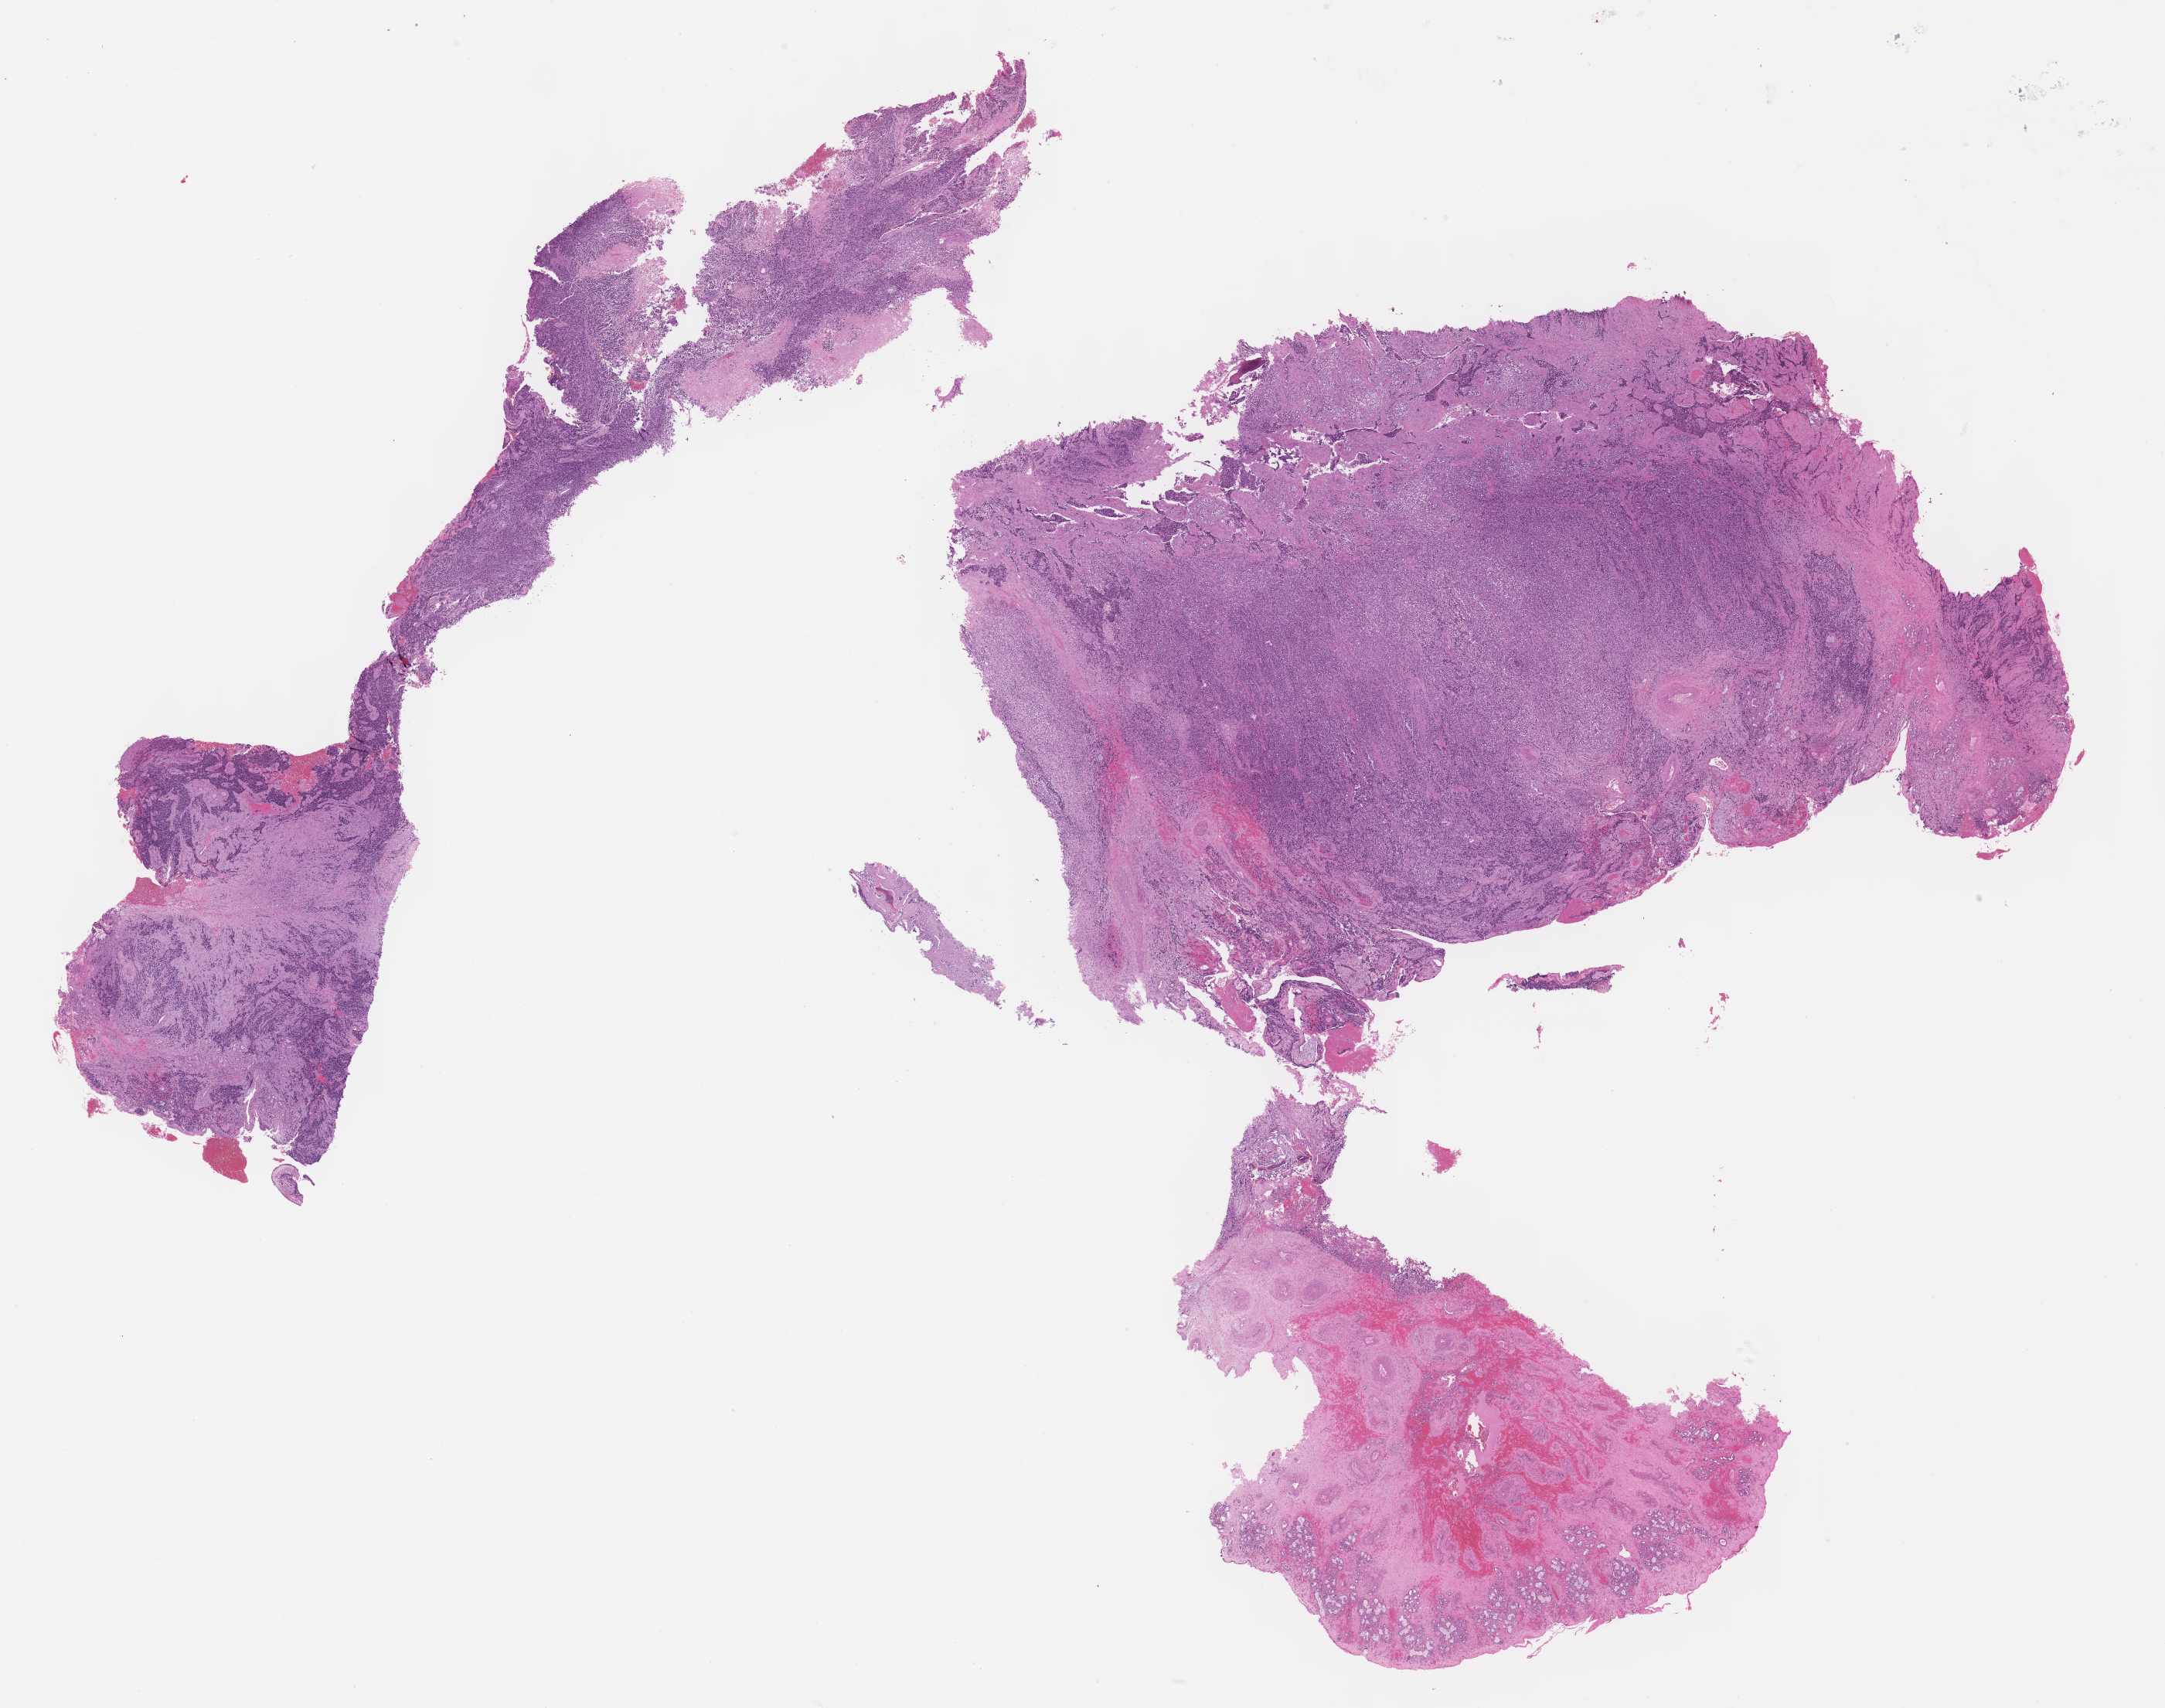
H&E whole-slide image of tumor tissue — a low-resolution overview of the entire scanned area, about 22.6 x 17.9 mm, formalin-fixed, paraffin-embedded (FFPE) tissue, site: soft tissue, cheek-left. Patient: male, age 37.8 years at diagnosis.
Diagnosis: rhabdomyosarcoma; histological classification: alveolar rhabdomyosarcoma.